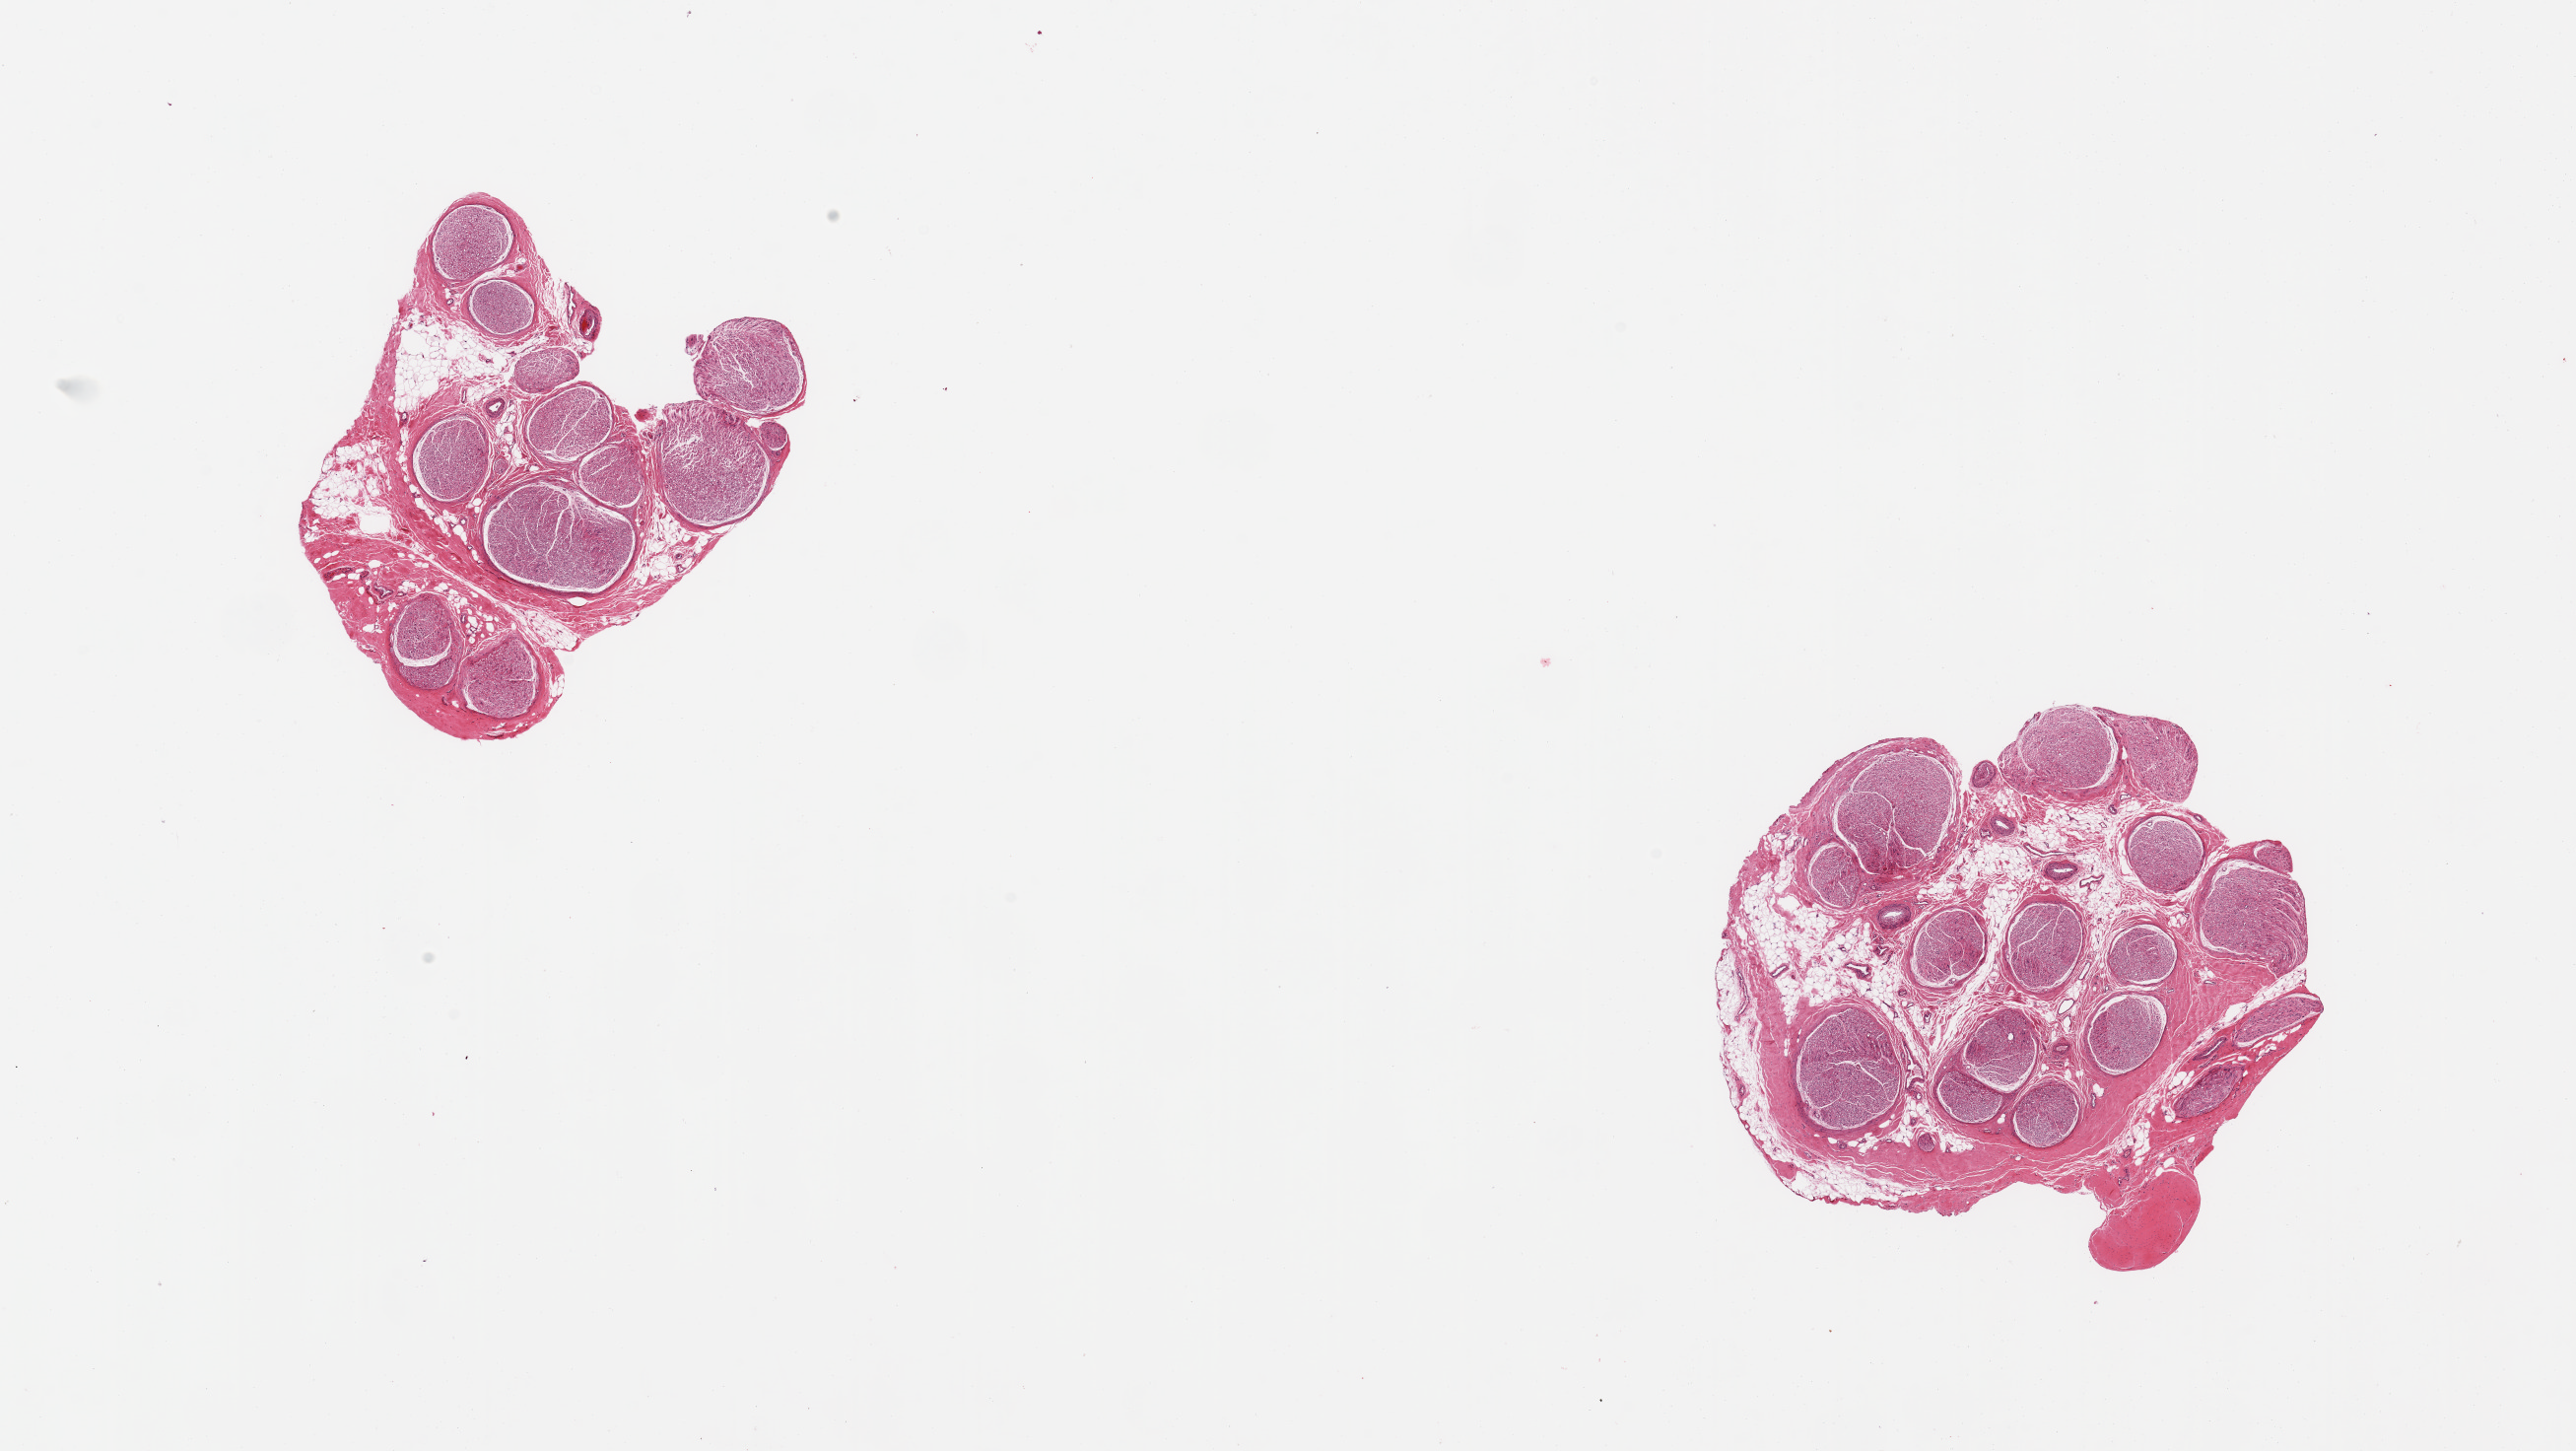
Hematoxylin and eosin (H&E) whole-slide image, low-resolution overview of the scanned area, about 20.7 x 11.6 mm (from a 20x scan). PAXgene-fixed, paraffin-embedded tissue. Sampled site (target tissue): tibial nerve. Tissue donor sample. Male donor.
• pathologist's review note for this sample: 2 pieces, partial fibrous rim up to ~0.5mm